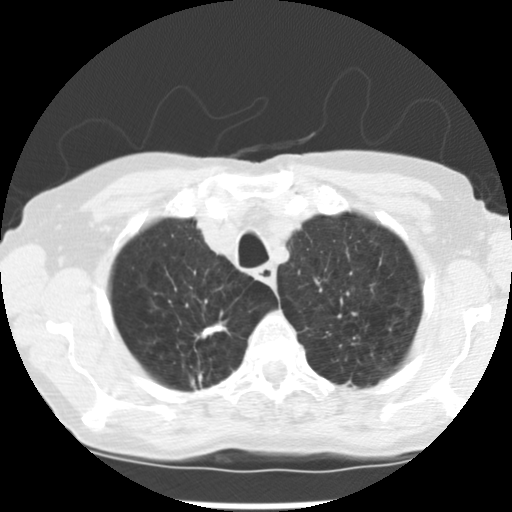
Axial slice from a low-dose chest CT screening exam. Baseline annual screen. Lung window (W 1500 / L -600 HU). 2.5 mm slice thickness. Standard (soft-tissue) reconstruction kernel (STANDARD). 120 kVp. Slice 37 of 265 in the series. 512 × 512 image matrix, field of view 300 × 300 mm. Female, age 72 years at enrolment.
Expert reader's lesion annotation, bounding box [x1, y1, x2, y2] px = [182, 311, 232, 350]. The screening reader recorded 3 non-calcified nodules or masses ≥4 mm on this exam (right upper lobe, left upper lobe, left lower lobe); which of them this box marks is not recorded. Participant outcome: lung cancer diagnosed 50 days after this screen — adenocarcinoma, NOS, right upper lobe, moderately differentiated (G2), stage IB (AJCC 6th edition), 22 mm at pathology.